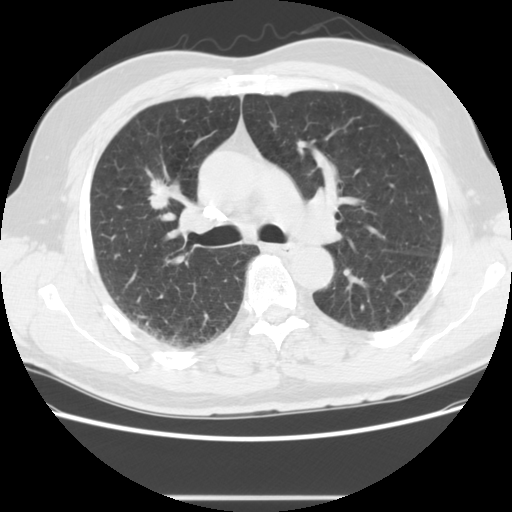
Low-dose screening chest CT, axial slice. Second annual screen. Lung window (W 1500 / L -600 HU). Standard (soft-tissue) reconstruction kernel (STANDARD). Slice 54 of 139 in the series. 512 × 512 image matrix. Male, age 59 years at enrolment.
• Expert reader's lesion annotation, box from (x=137, y=175) to (x=178, y=217) px.
• The exam's reader record, not a measurement of the box and not confirmed to be the same lesion: non-calcified nodule or mass ≥4 mm, right upper lobe, 20 × 13 mm, spiculated (stellate) margins, soft tissue attenuation, pre-existing on the prior screen: yes; interval growth: yes.
• Participant outcome: lung cancer diagnosed 267 days after this screen — large cell carcinoma, NOS, right upper lobe, poorly differentiated (G3), stage IIIA (AJCC 6th edition), 34 mm at pathology.